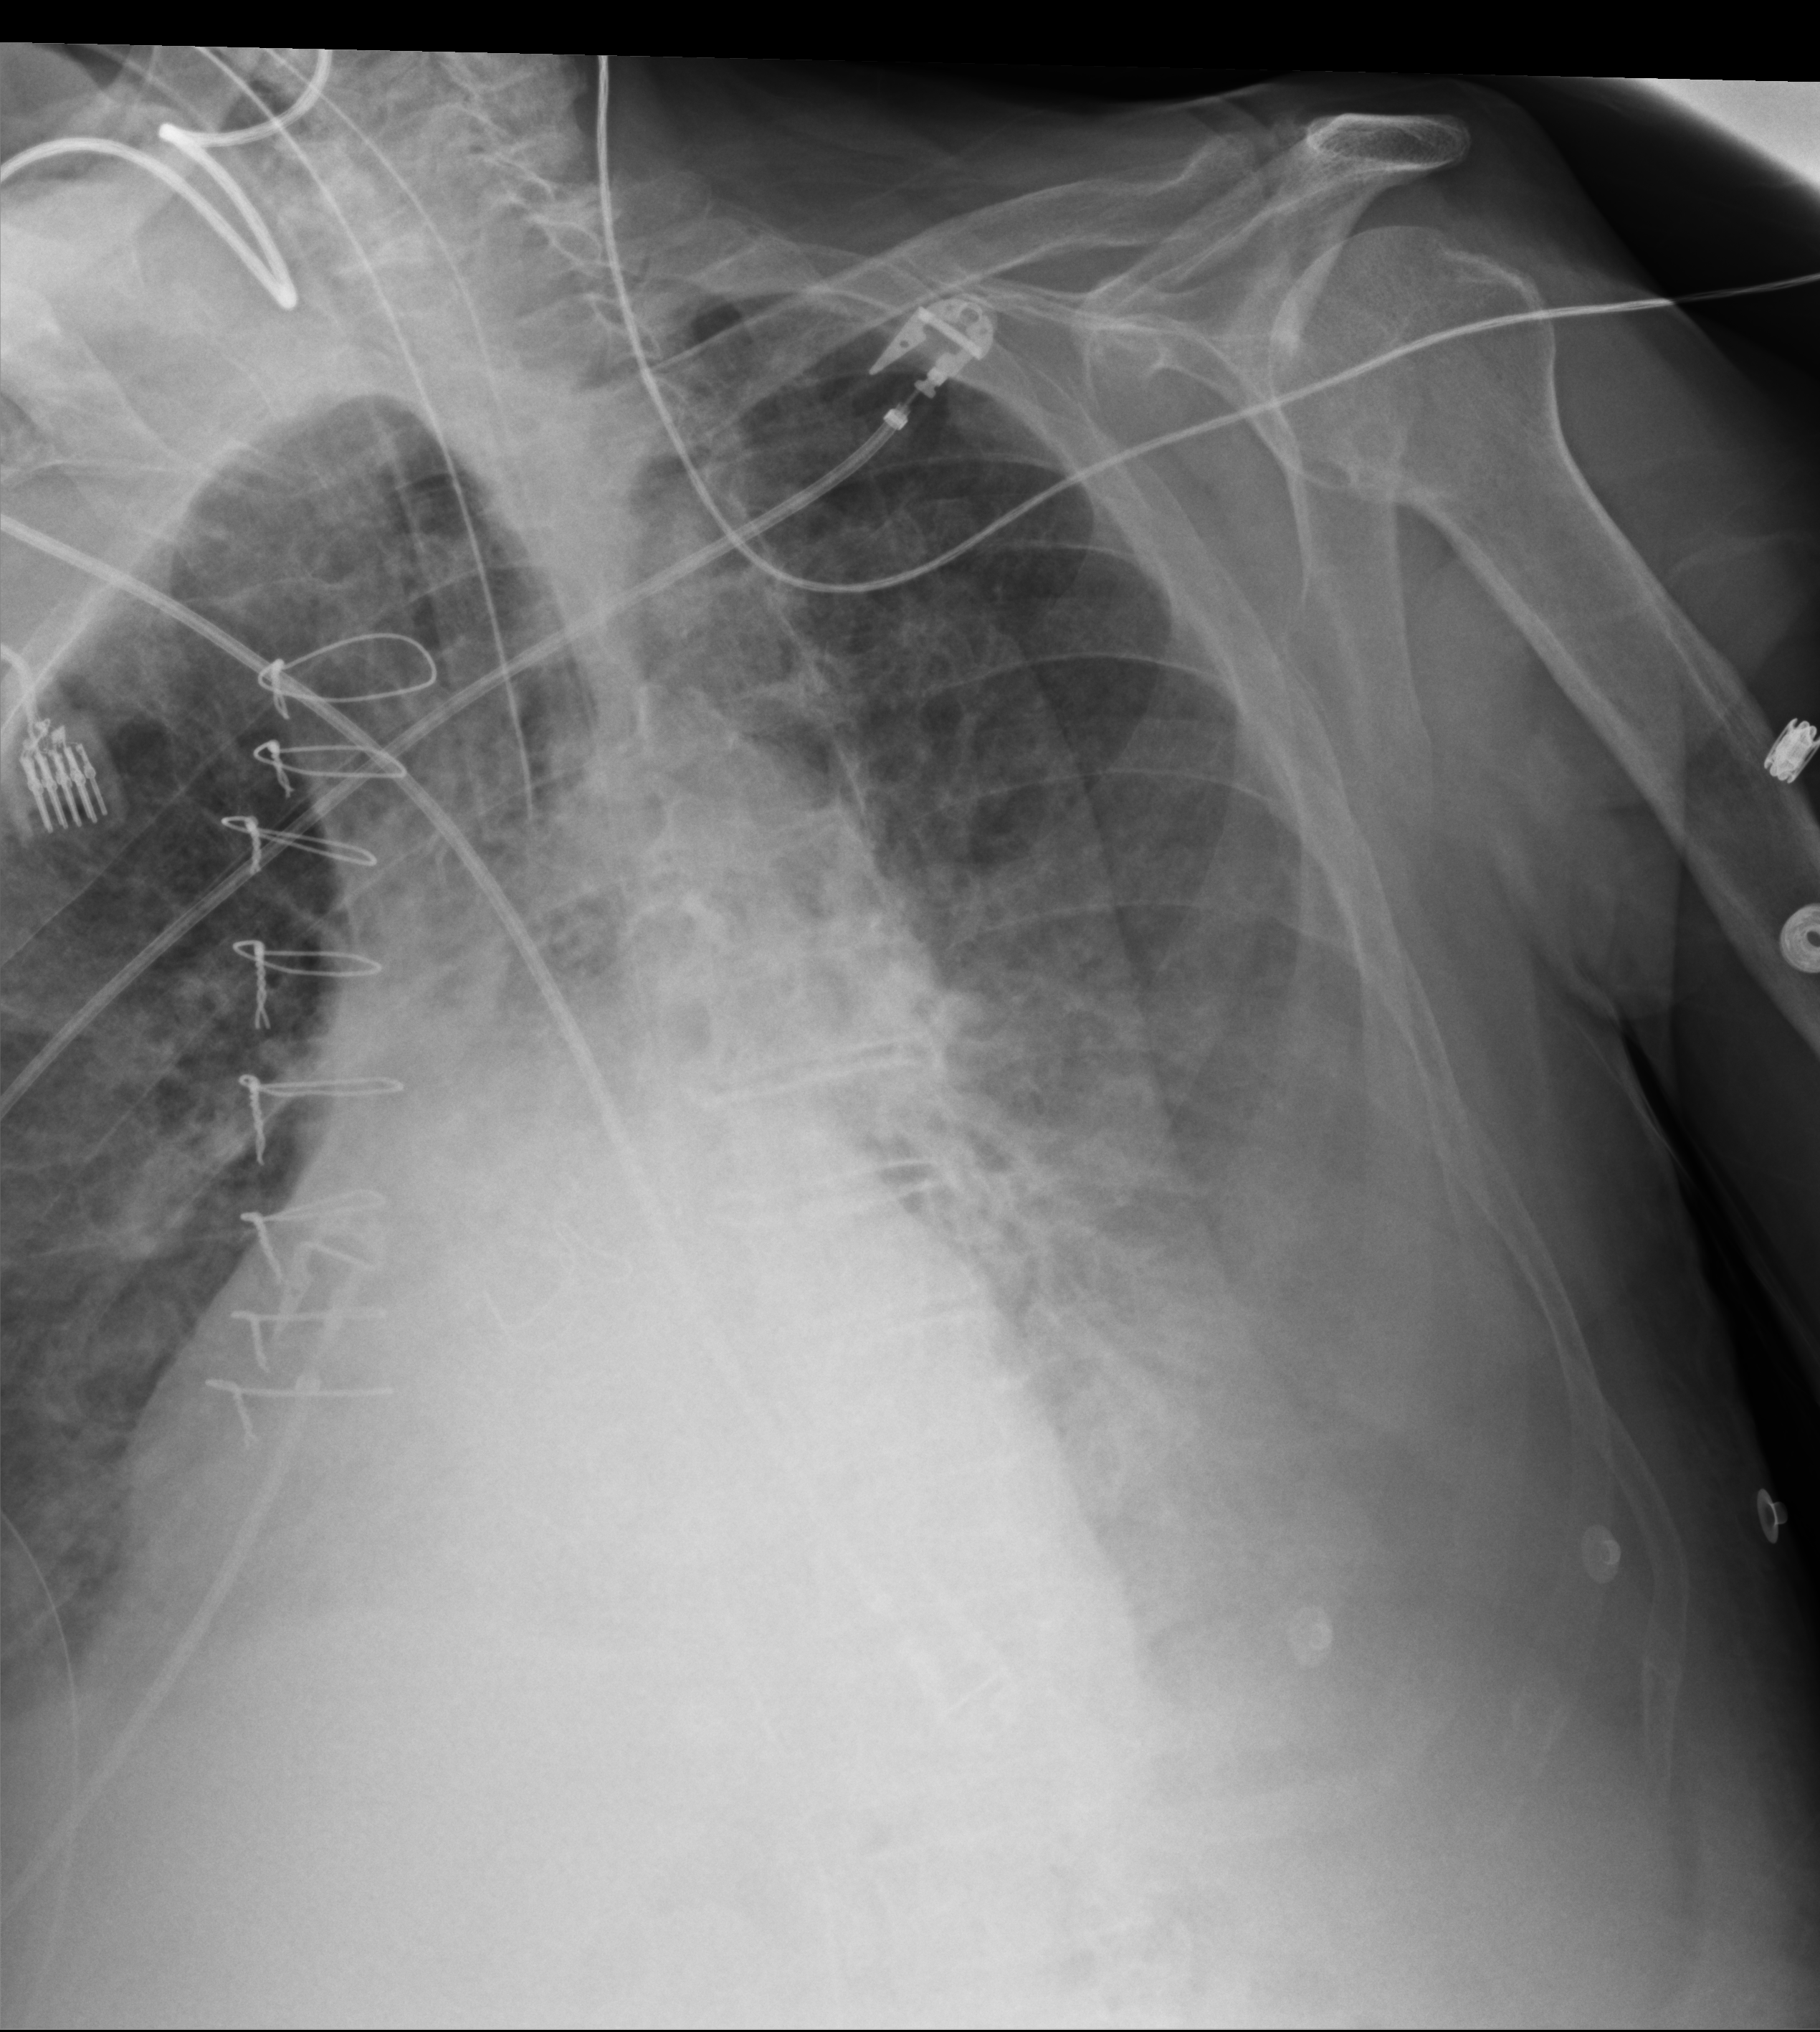
Chest X-ray (portable), anteroposterior (AP) projection. Patient hospitalised with COVID-19; male, aged 75–90 years.
Admission-level facts for this patient (not findings on this image; timing relative to this image not recorded): length of hospital stay: 40 days; admitted to intensive care during this hospital stay: yes; mechanically ventilated during this hospital stay: yes.